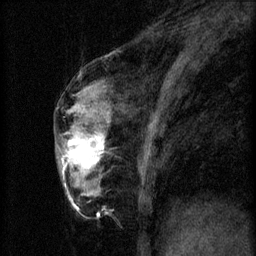
Breast MRI (dynamic contrast-enhanced), one sagittal slice. Position 26 of 60 along the scan axis. 3 images stored at this slice position (order not interpretable as contrast timing). 1.5 T. TE 4.2 ms, TR 8.2 ms. 2 mm slice thickness. 256 × 256 image matrix. Female patient, age 56 years.
Structures marked on this image (semi-automatically segmented with operator editing):
- analysis volume of interest (the breast-tissue region the enhancement analysis was run in; not a lesion): bounding box (x1, y1, x2, y2) in pixels: (60, 124, 108, 179)
- tumour enhancement mask (voxels above the 70 % enhancement threshold inside the analysis volume of interest): (62, 132, 105, 169)